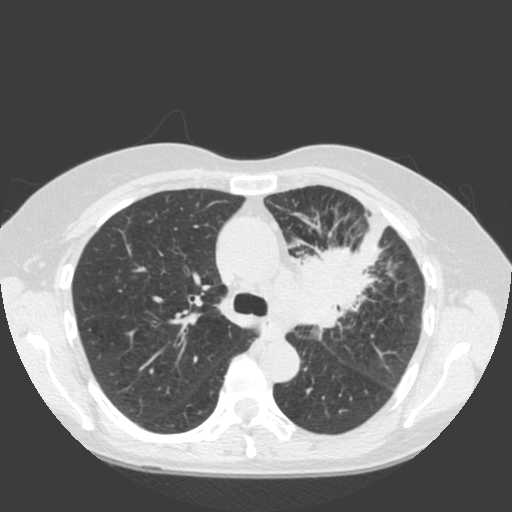
Low-dose screening chest CT, one axial slice; position 129 of 184 along the scan axis; 120 kVp; lung window (W 1500 / L -600 HU); 2 mm slice thickness; 512 × 512 image matrix, field of view 350 × 350 mm.
Outlined on this slice (expert manual segmentation):
- lesion 1 (tumor, hilum of left lung): box from (x=294, y=208) to (x=387, y=327) px